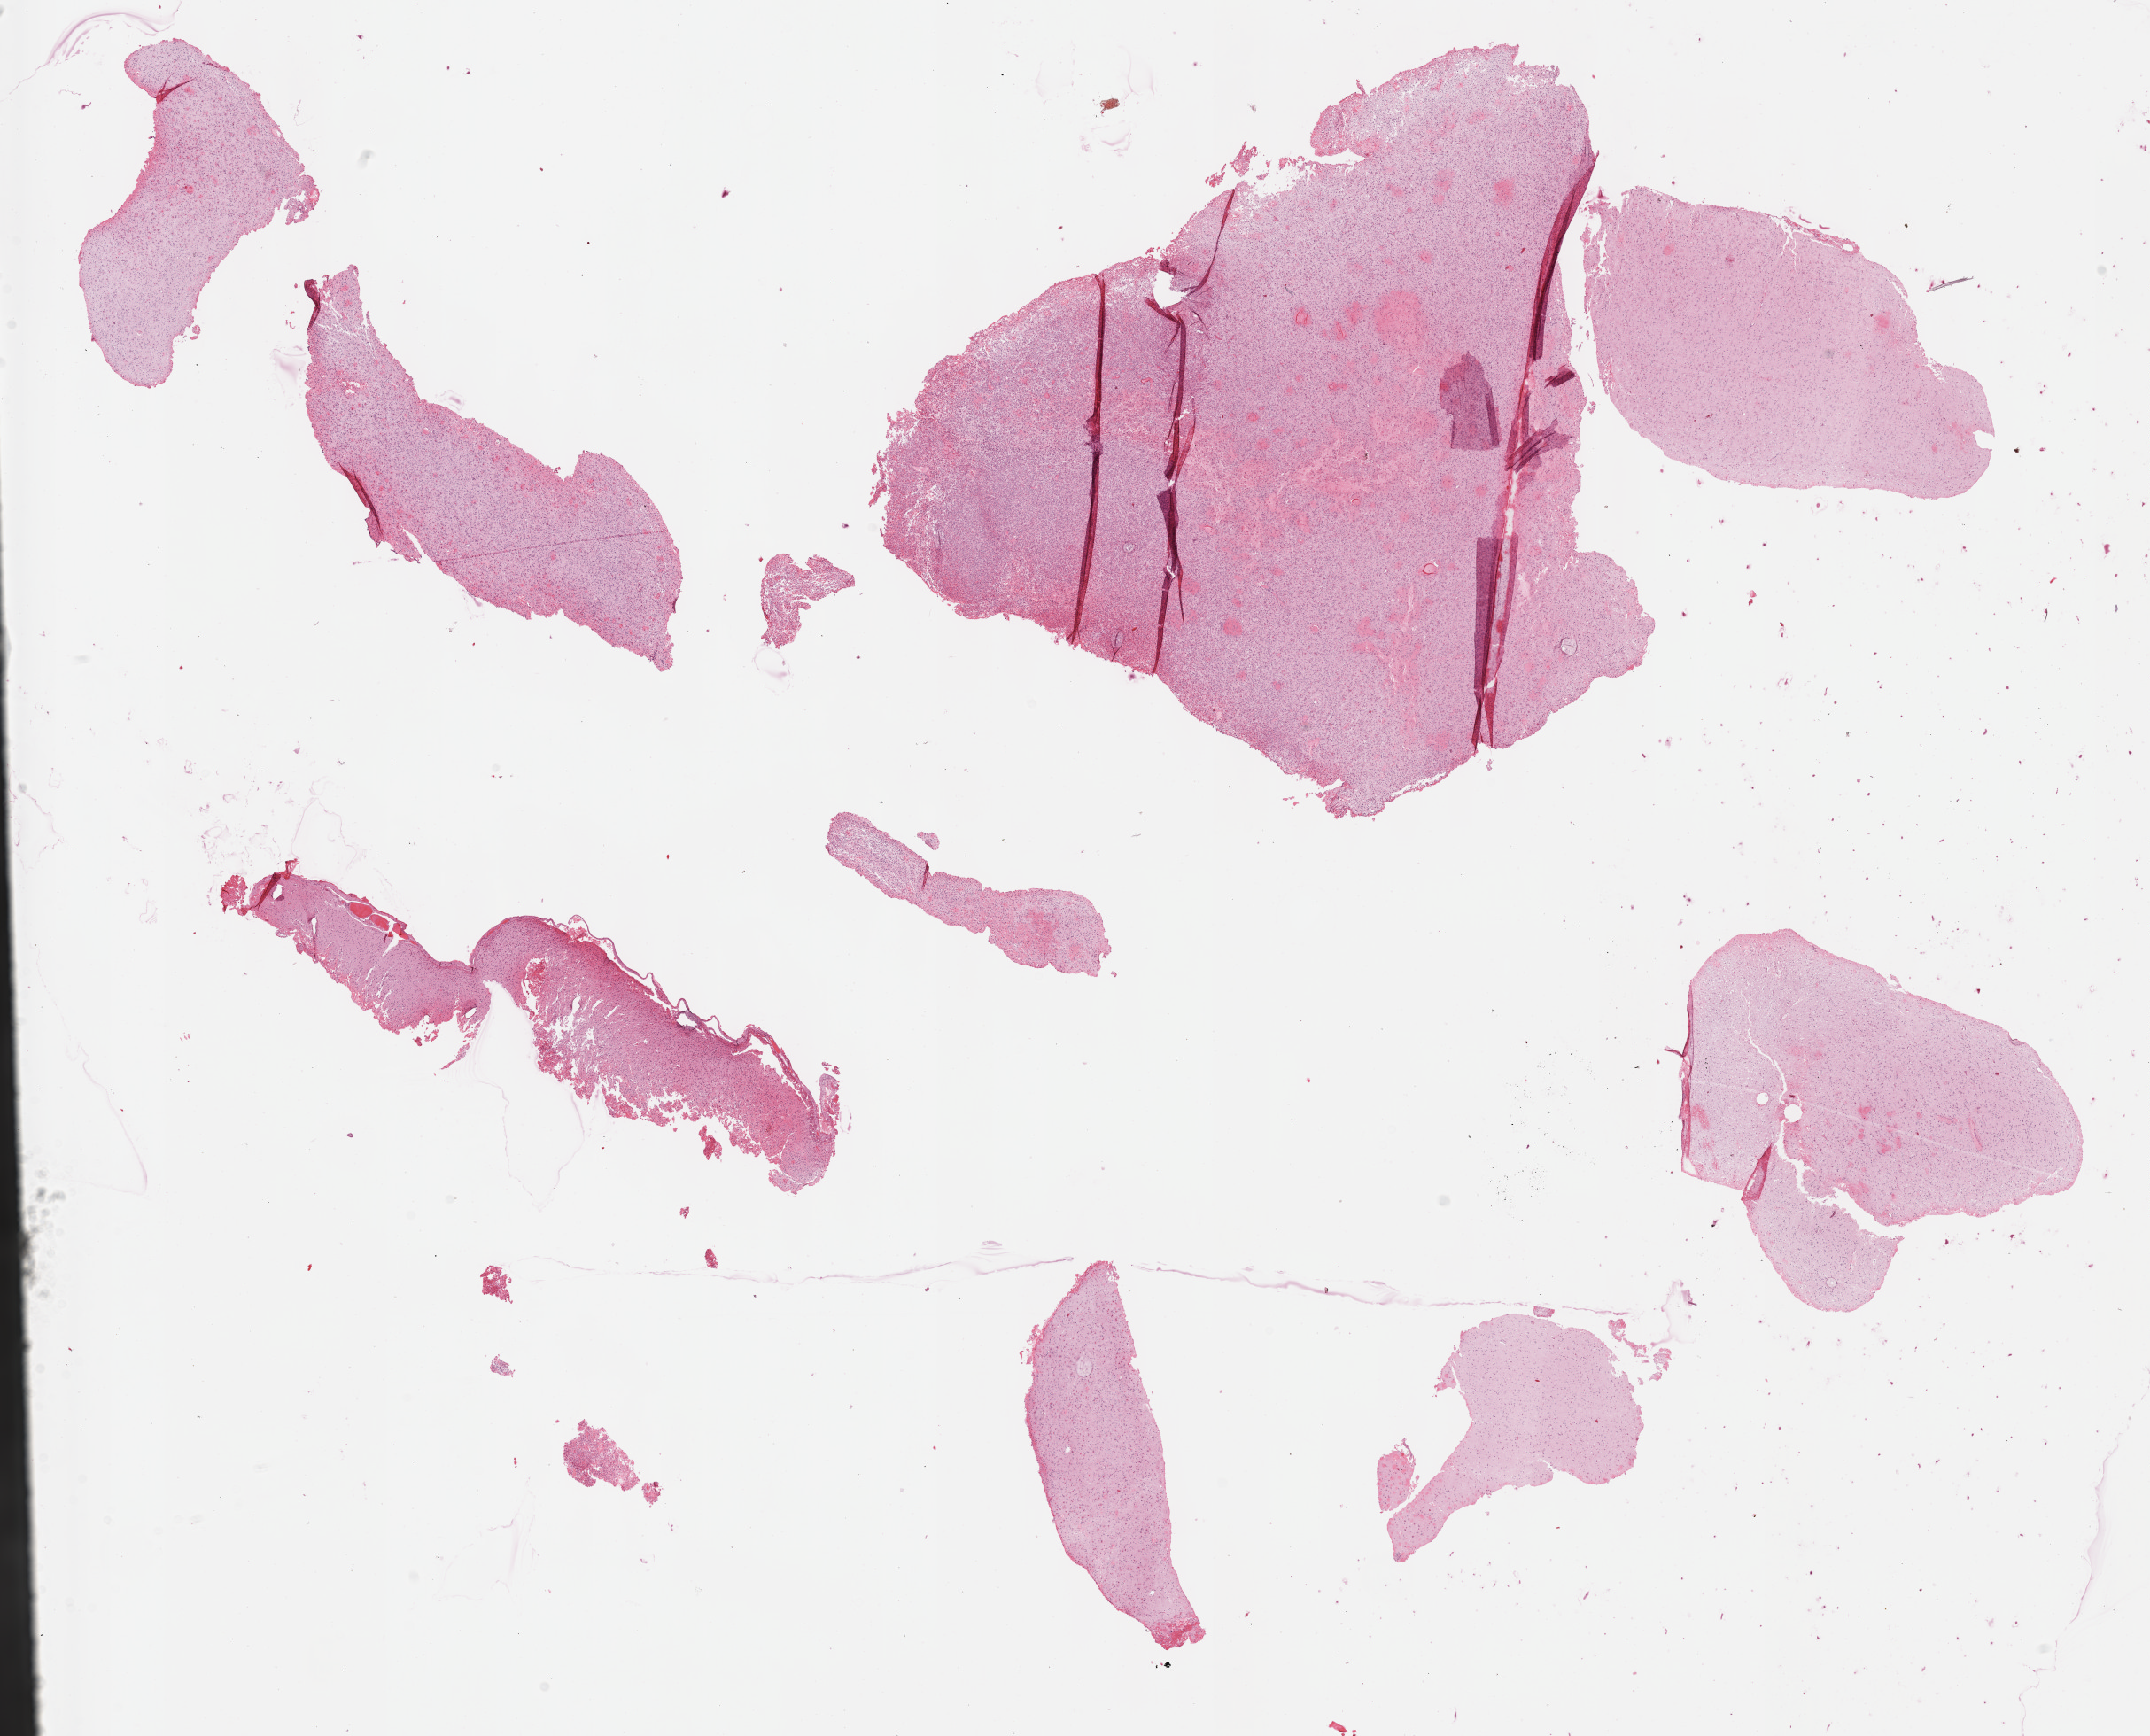
Whole-slide histology image, Hematoxylin and eosin (H&E) stained, shown as a low-resolution overview of the whole scanned area (about 19.6 x 15.9 mm); formalin-fixed paraffin-embedded (FFPE) diagnostic section; brain, primary tumour sample. Male patient; age at initial diagnosis 48 years. Histologic grade: G3 (poorly differentiated).
• diagnosis: Astrocytoma, anaplastic (cerebrum)